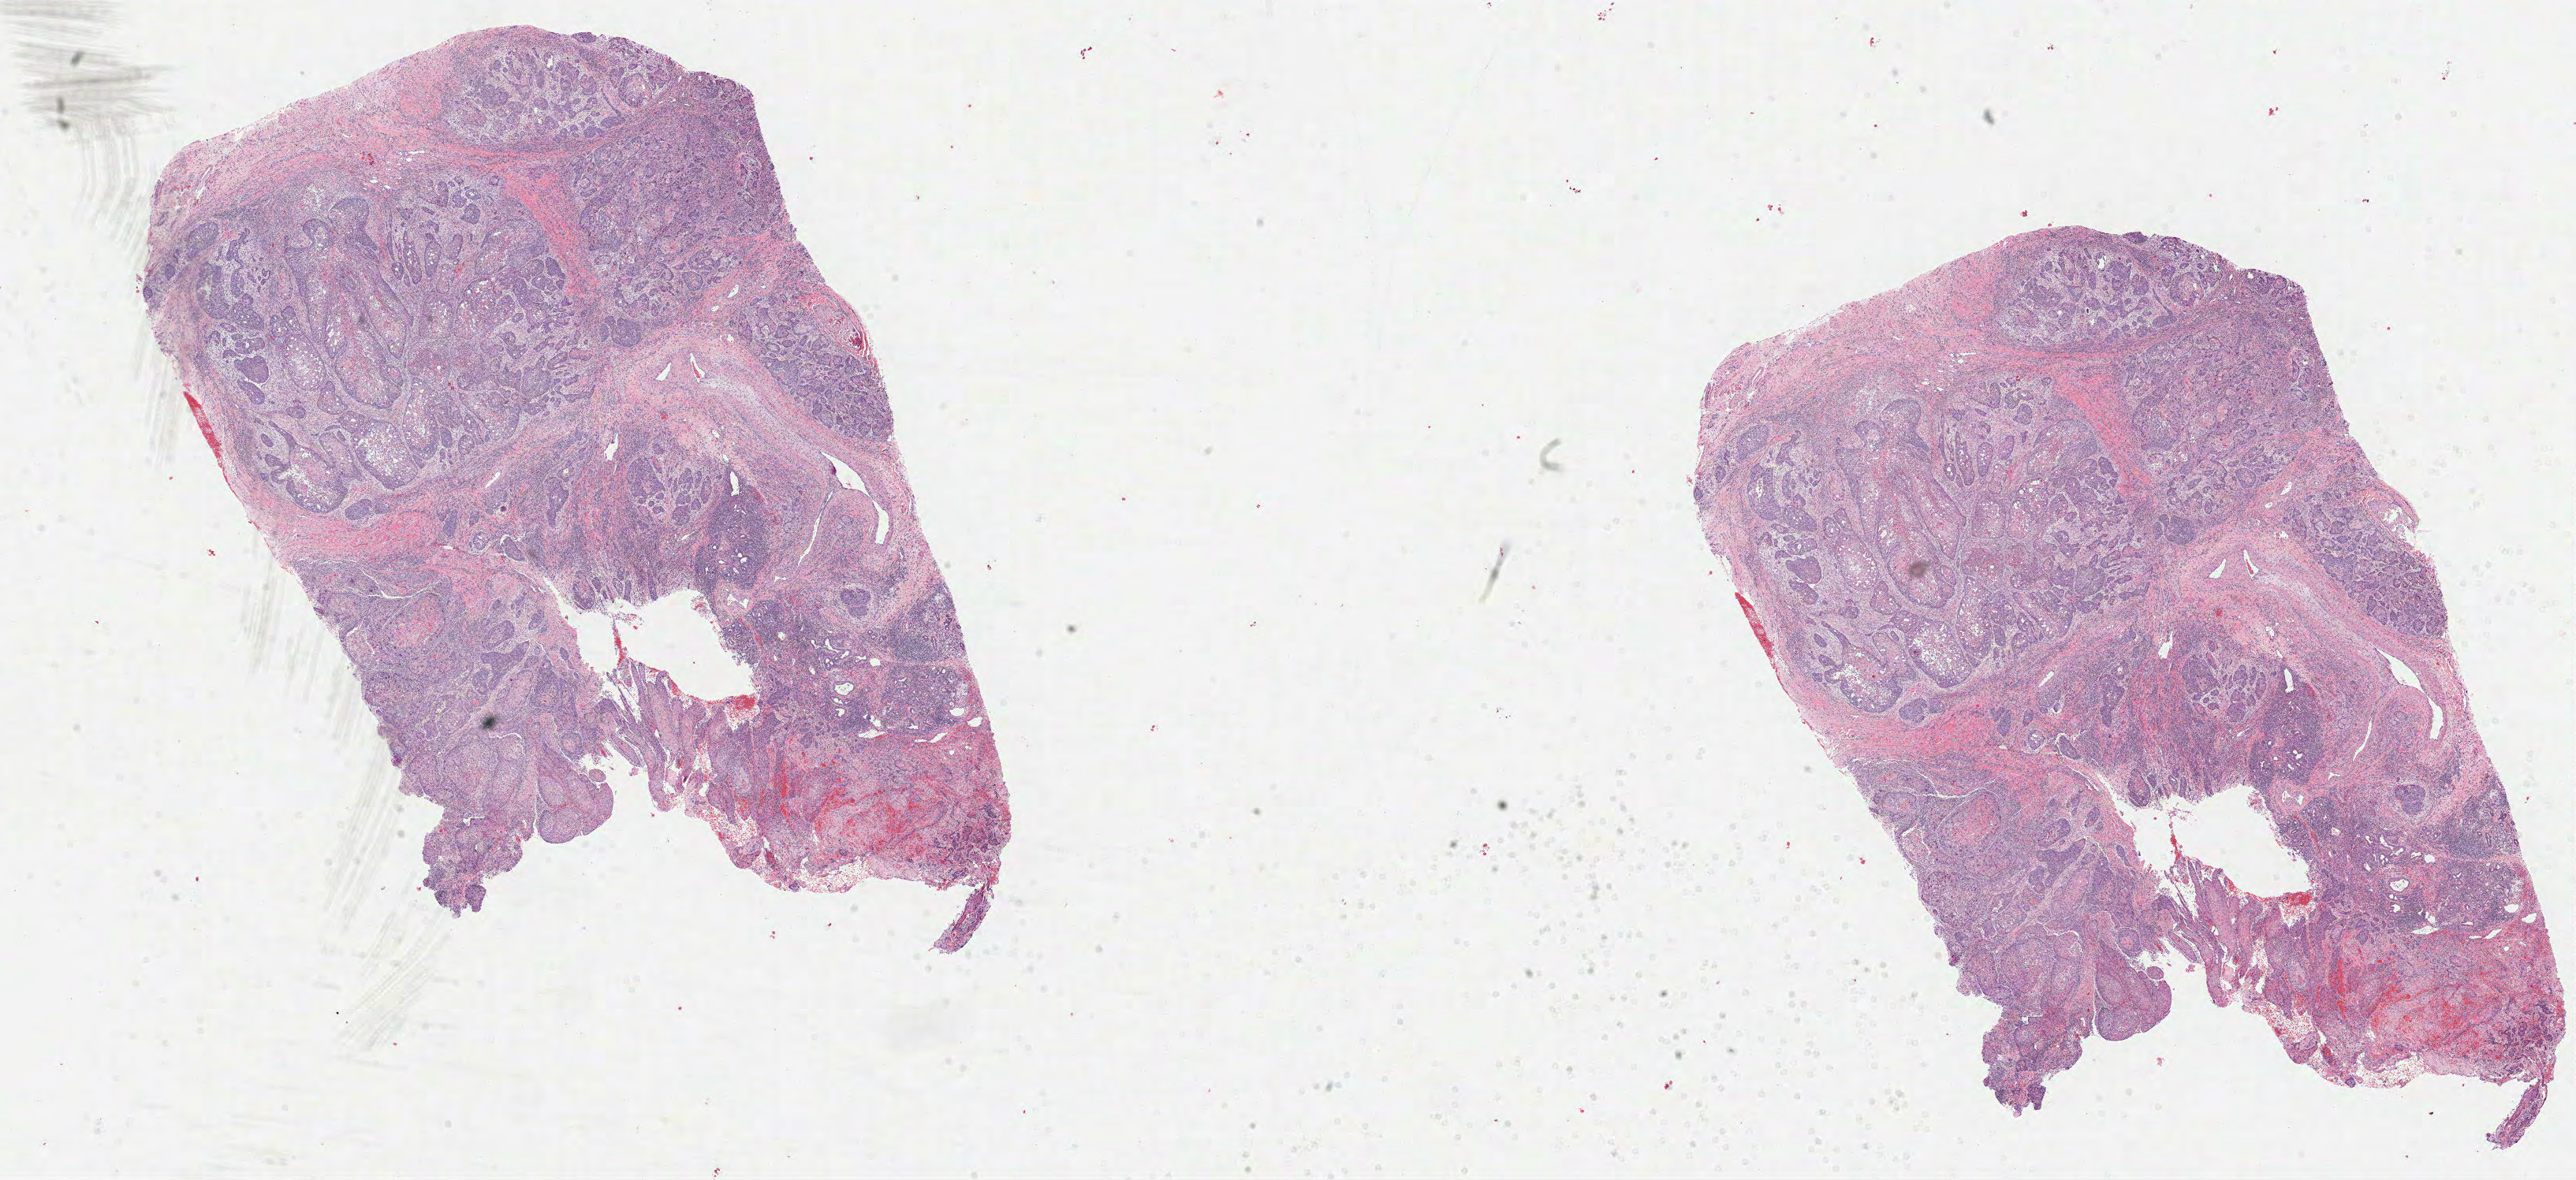
Whole-slide histology image, H&E-stained, low-resolution overview of the scanned area, about 26.3 x 12.1 mm. Formalin-fixed paraffin-embedded (FFPE) diagnostic section. Sample: primary tumour, head and neck. Patient: female, age at initial diagnosis 61 years. Histologic grade: G1 (well differentiated).
* diagnosis: Squamous cell carcinoma, NOS
* AJCC pathologic stage: II (7th edition)